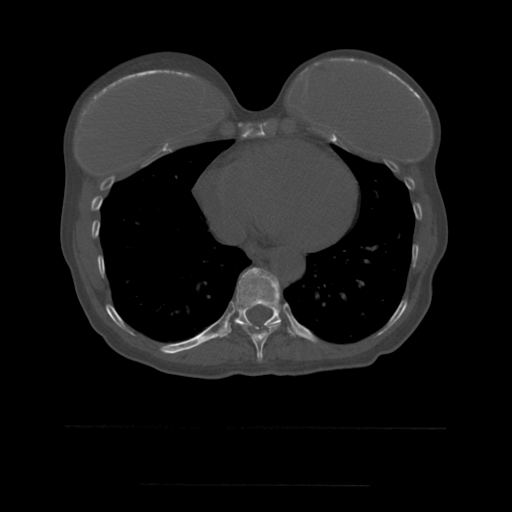
CT including the spine, one axial slice; slice 311 of 544 in the series (ordered by position); bone window (W 1800 / L 400 HU); 1.25 mm slice thickness; 512 × 512 image matrix, field of view 350 × 350 mm. Patient age 58 years. From the clinical record (not read from this slice): primary cancer: lung.
Outlined on this slice (semi-automatic segmentation, software-assisted and operator-edited):
- T10 vertebra: bounding box [x1, y1, x2, y2] px = [217, 268, 296, 338]
- T9 vertebra: [241, 322, 281, 361]